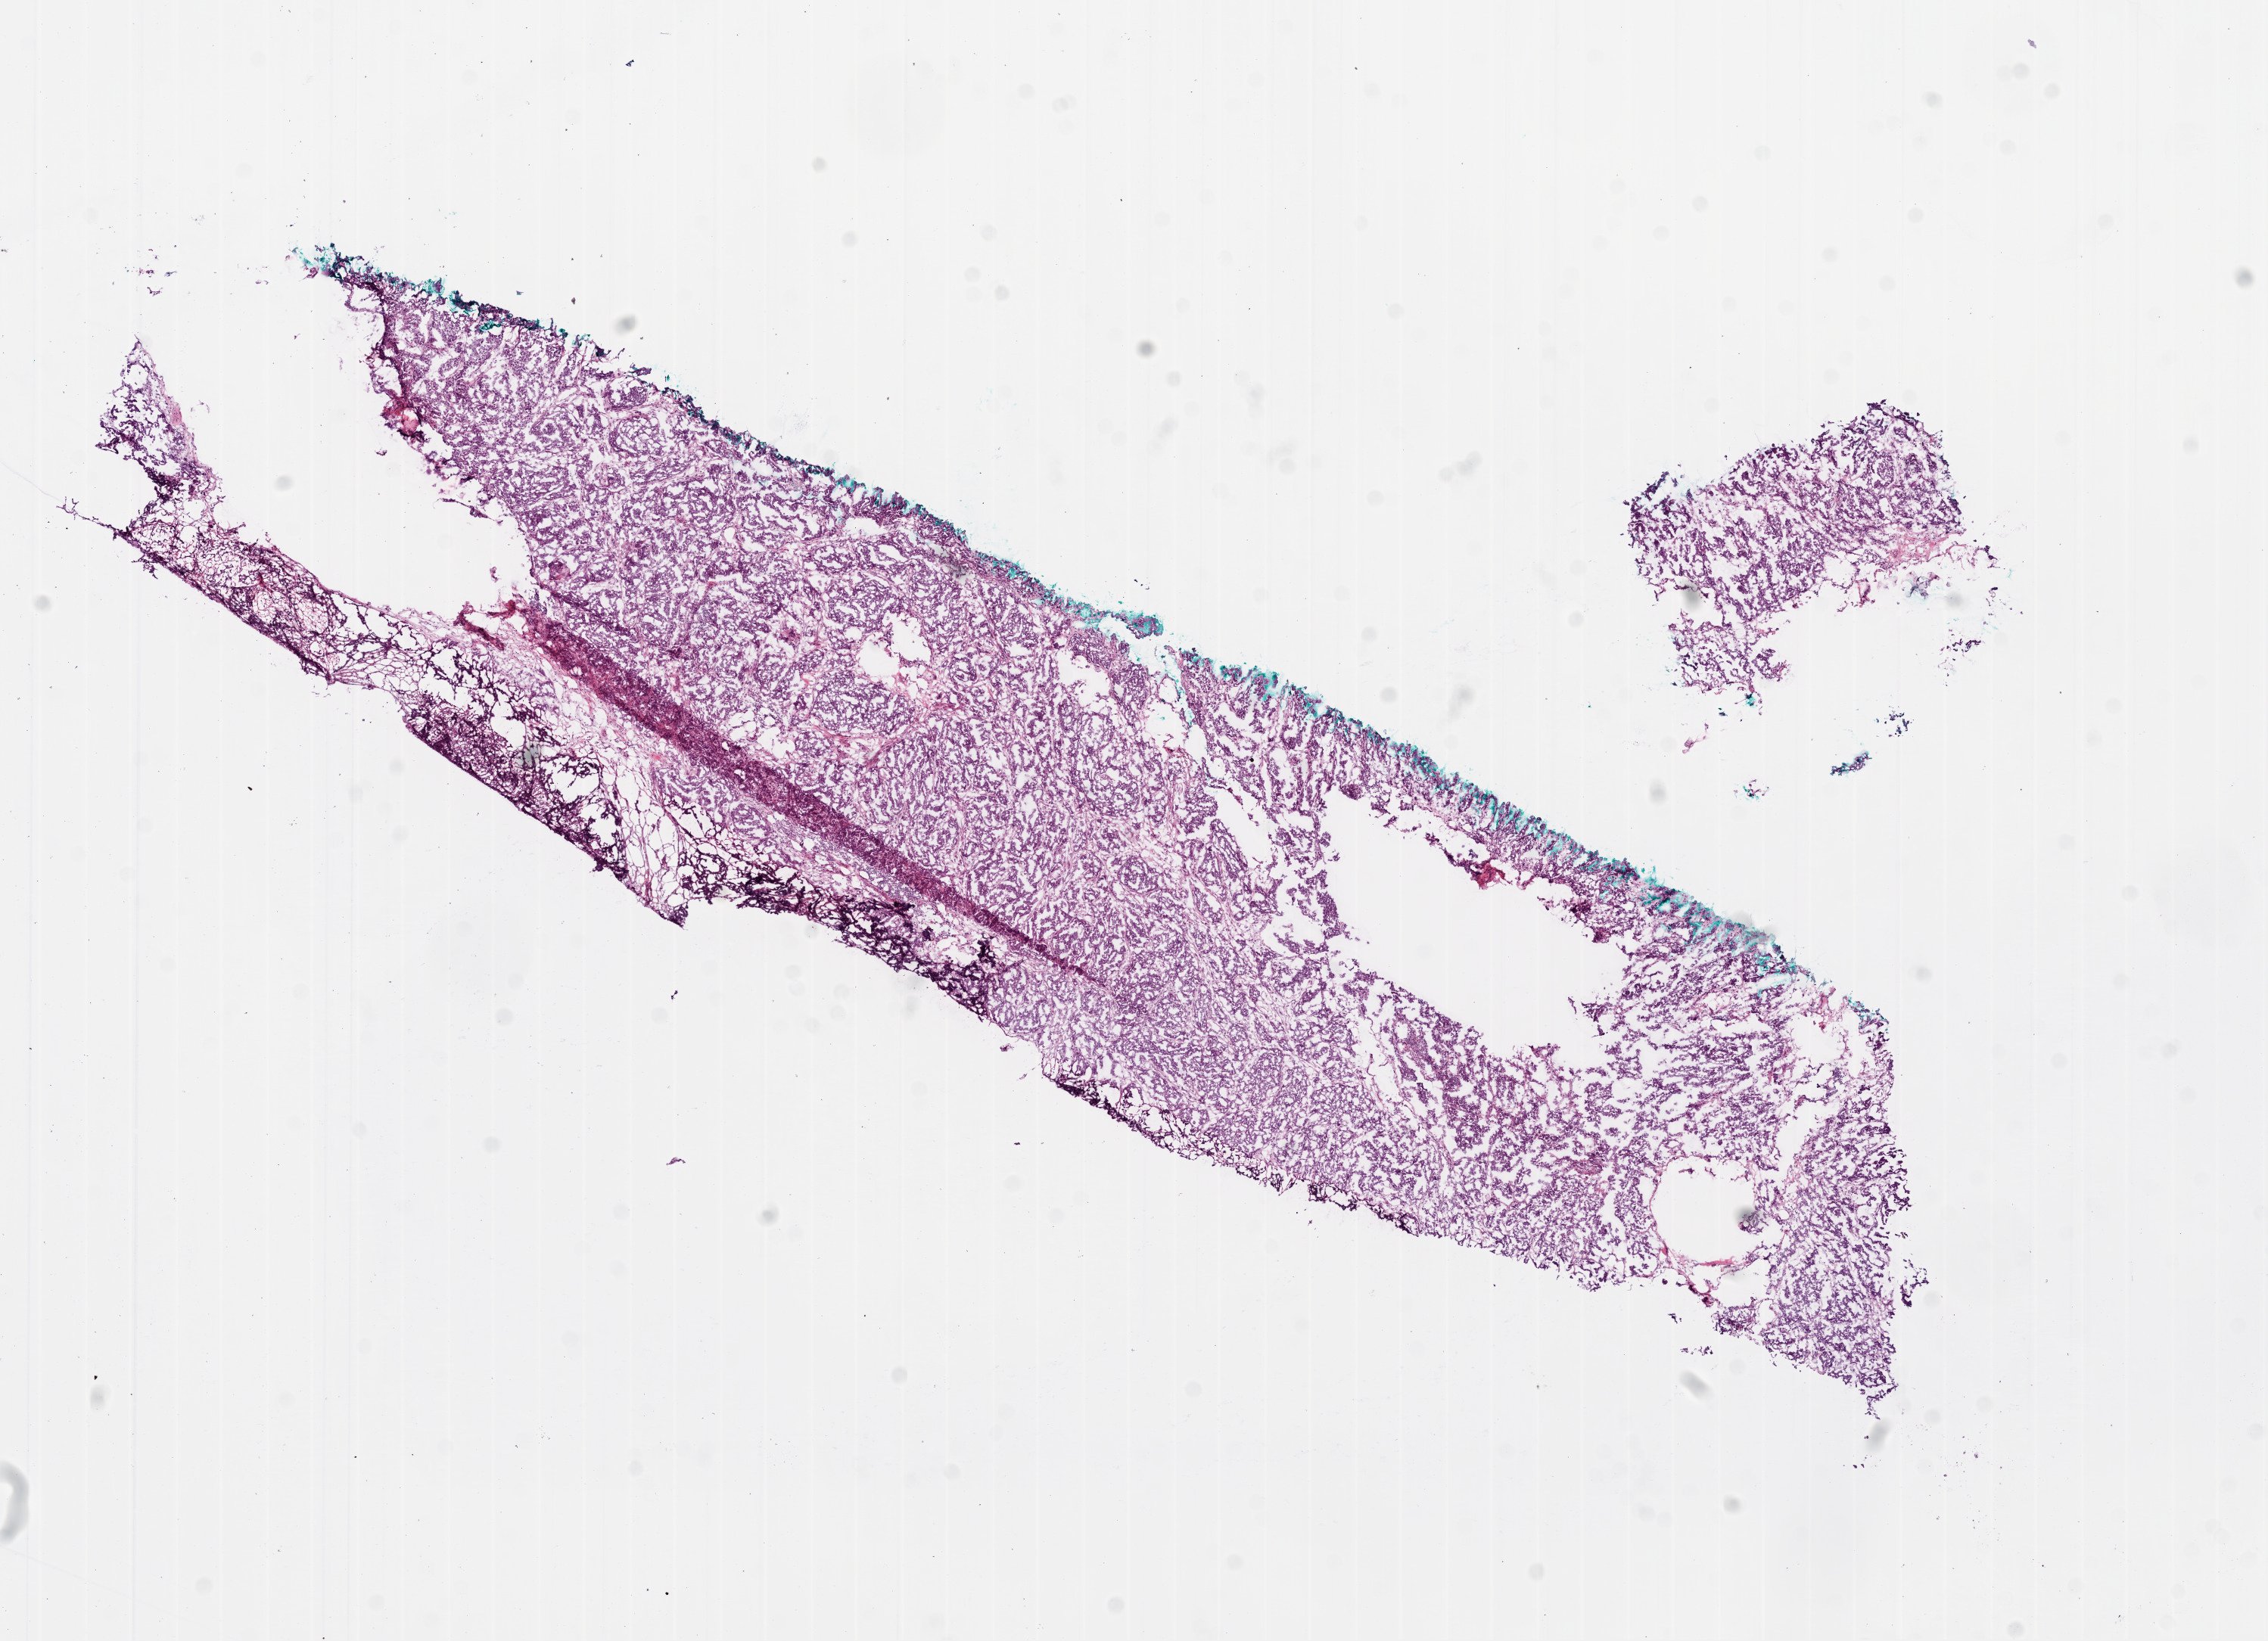
Hematoxylin and eosin (H&E) stained whole-slide image, low-resolution overview of the scanned area, about 12.1 x 8.7 mm. Frozen section from the bottom of the tissue portion. Sample: primary tumour, ovary. Female, age 55 years at initial diagnosis. Histologic grade: G3 (poorly differentiated). Pathologist review of this section (percent, as recorded): tumour cells 90%, tumour nuclei 91%, normal cells 9%, necrosis 1%.
Laterality: bilateral. FIGO stage: IV. Diagnosis: Serous cystadenocarcinoma, NOS.